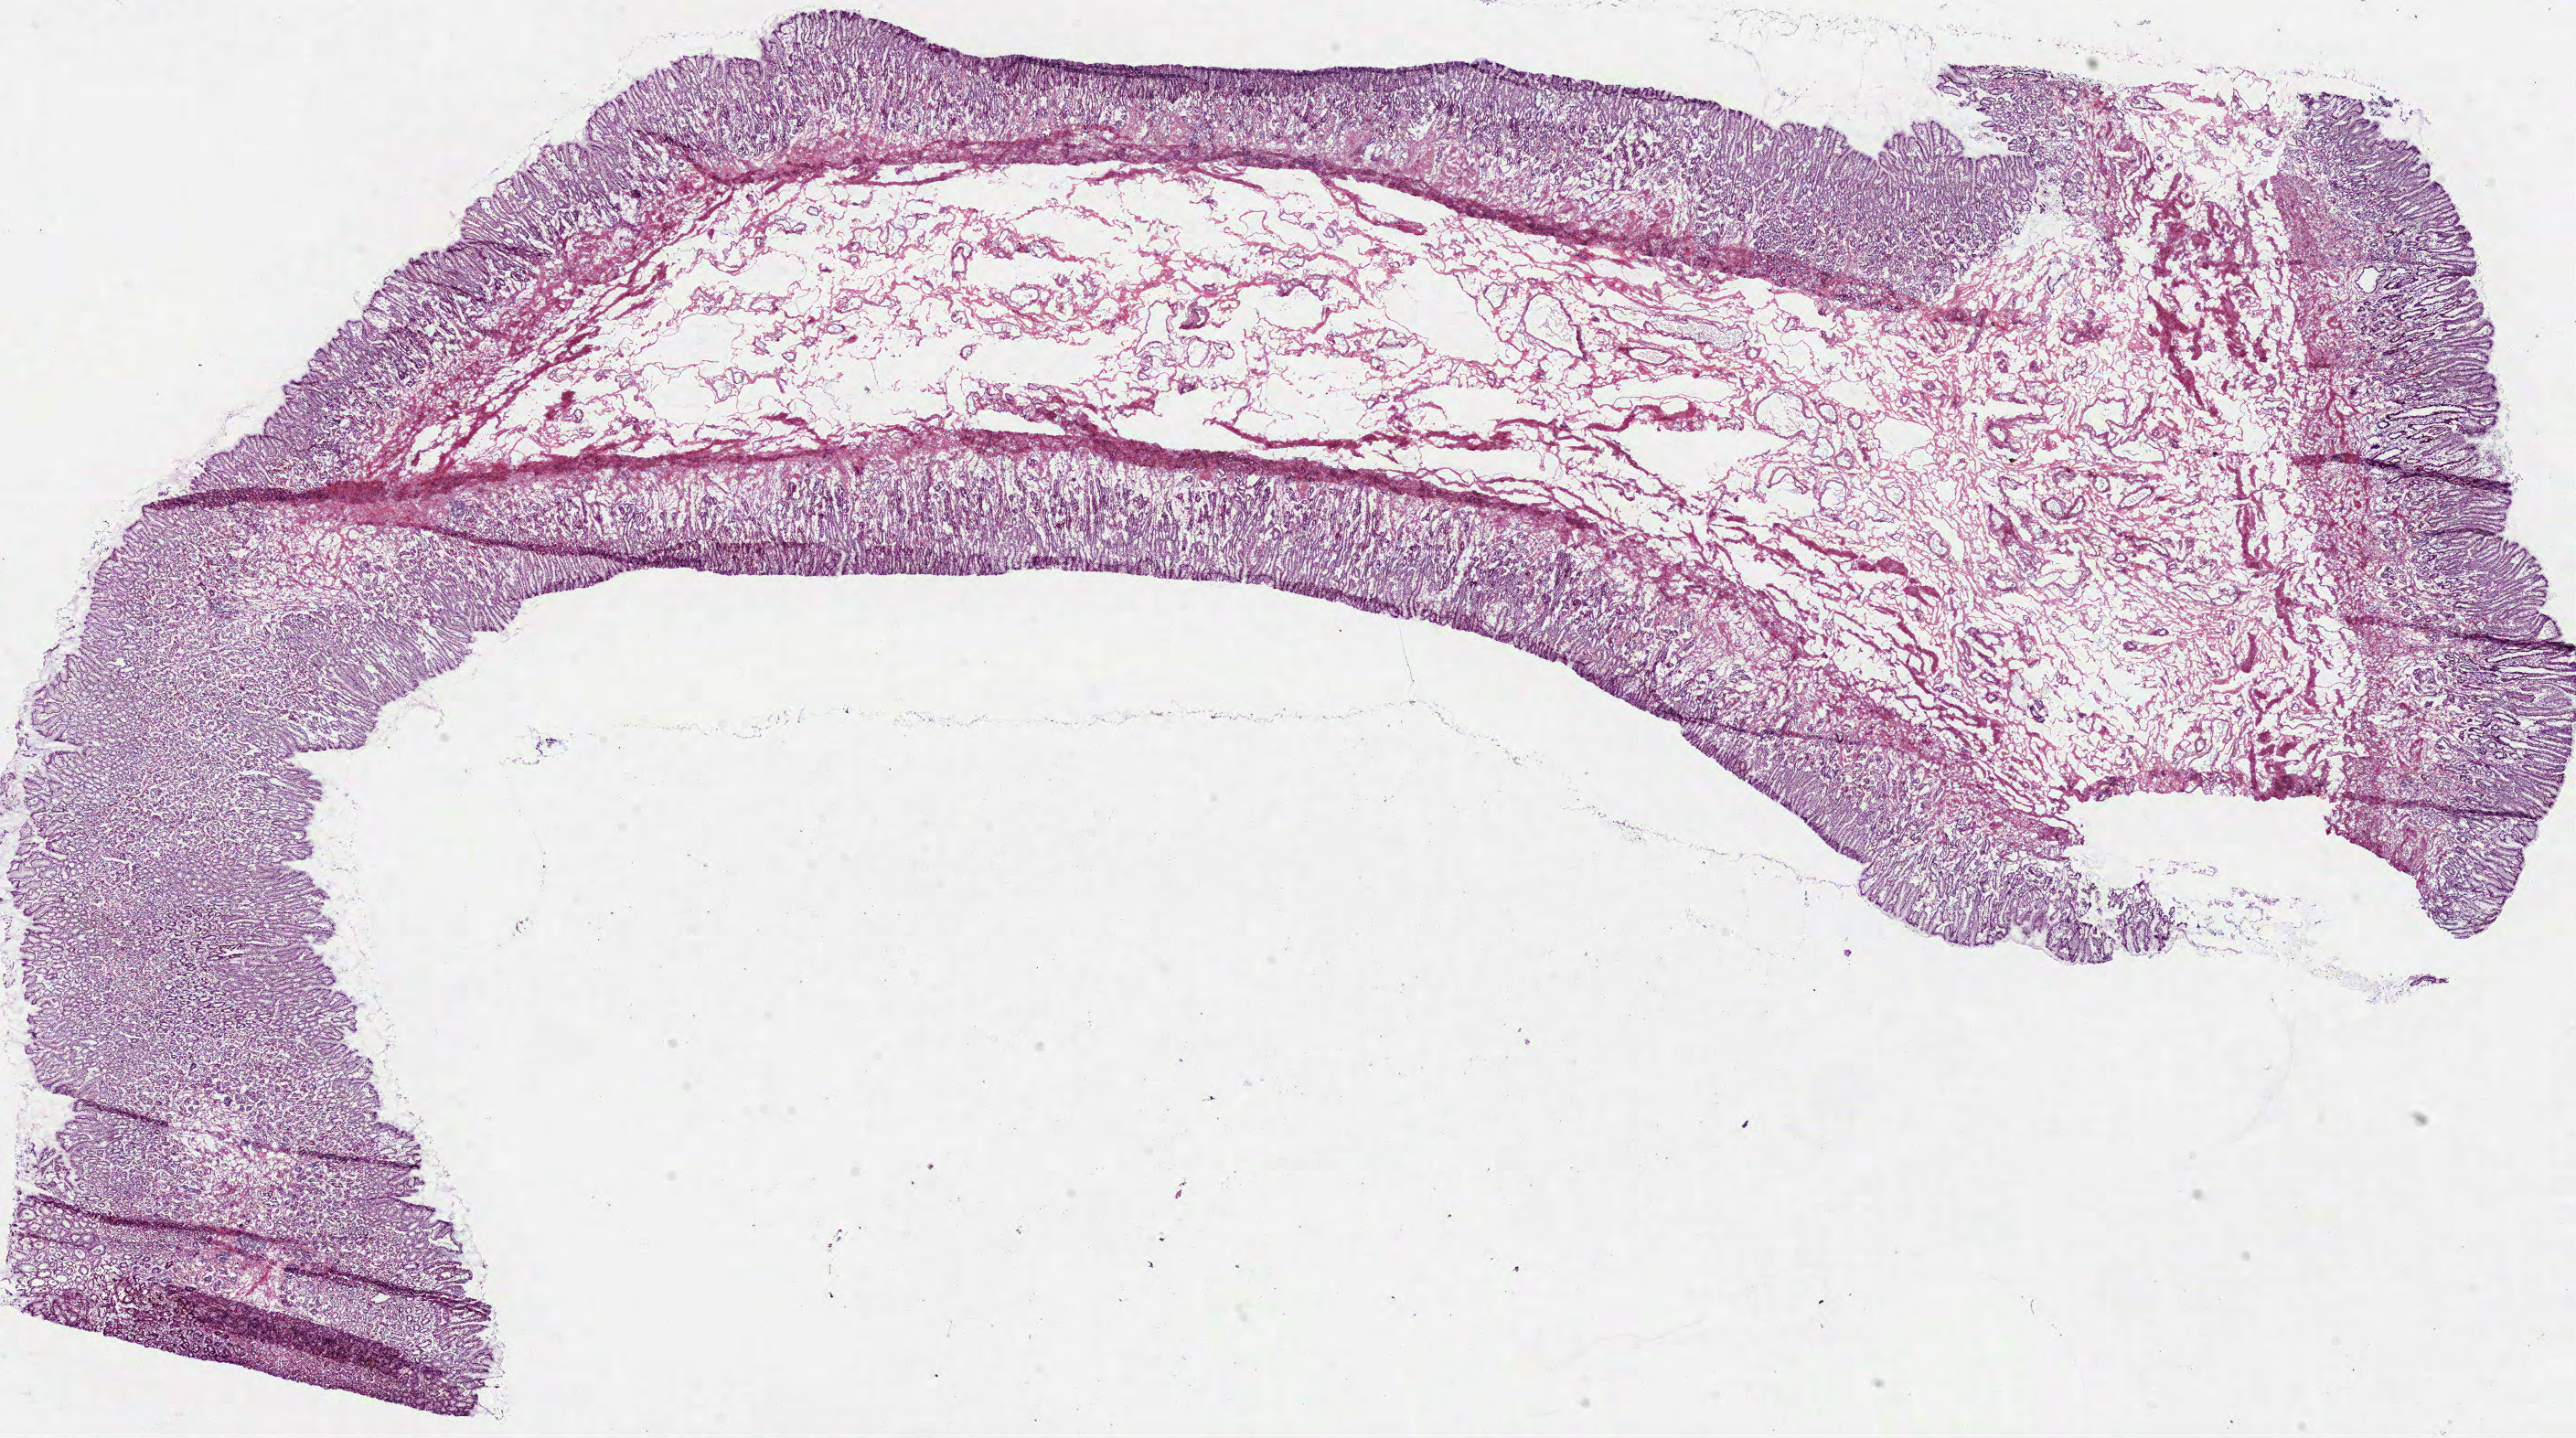
Digitized H&E tissue section (whole slide) — shown as a low-resolution overview of the whole scanned area (about 22.7 x 12.7 mm, from a 40x scan); frozen section; solid tissue normal (non-tumour tissue) sample from the stomach. Patient: male, age at initial diagnosis 65 years.
This section: solid tissue normal (non-tumour) sample from the same patient. Patient diagnosis: Adenocarcinoma, NOS (body of stomach).